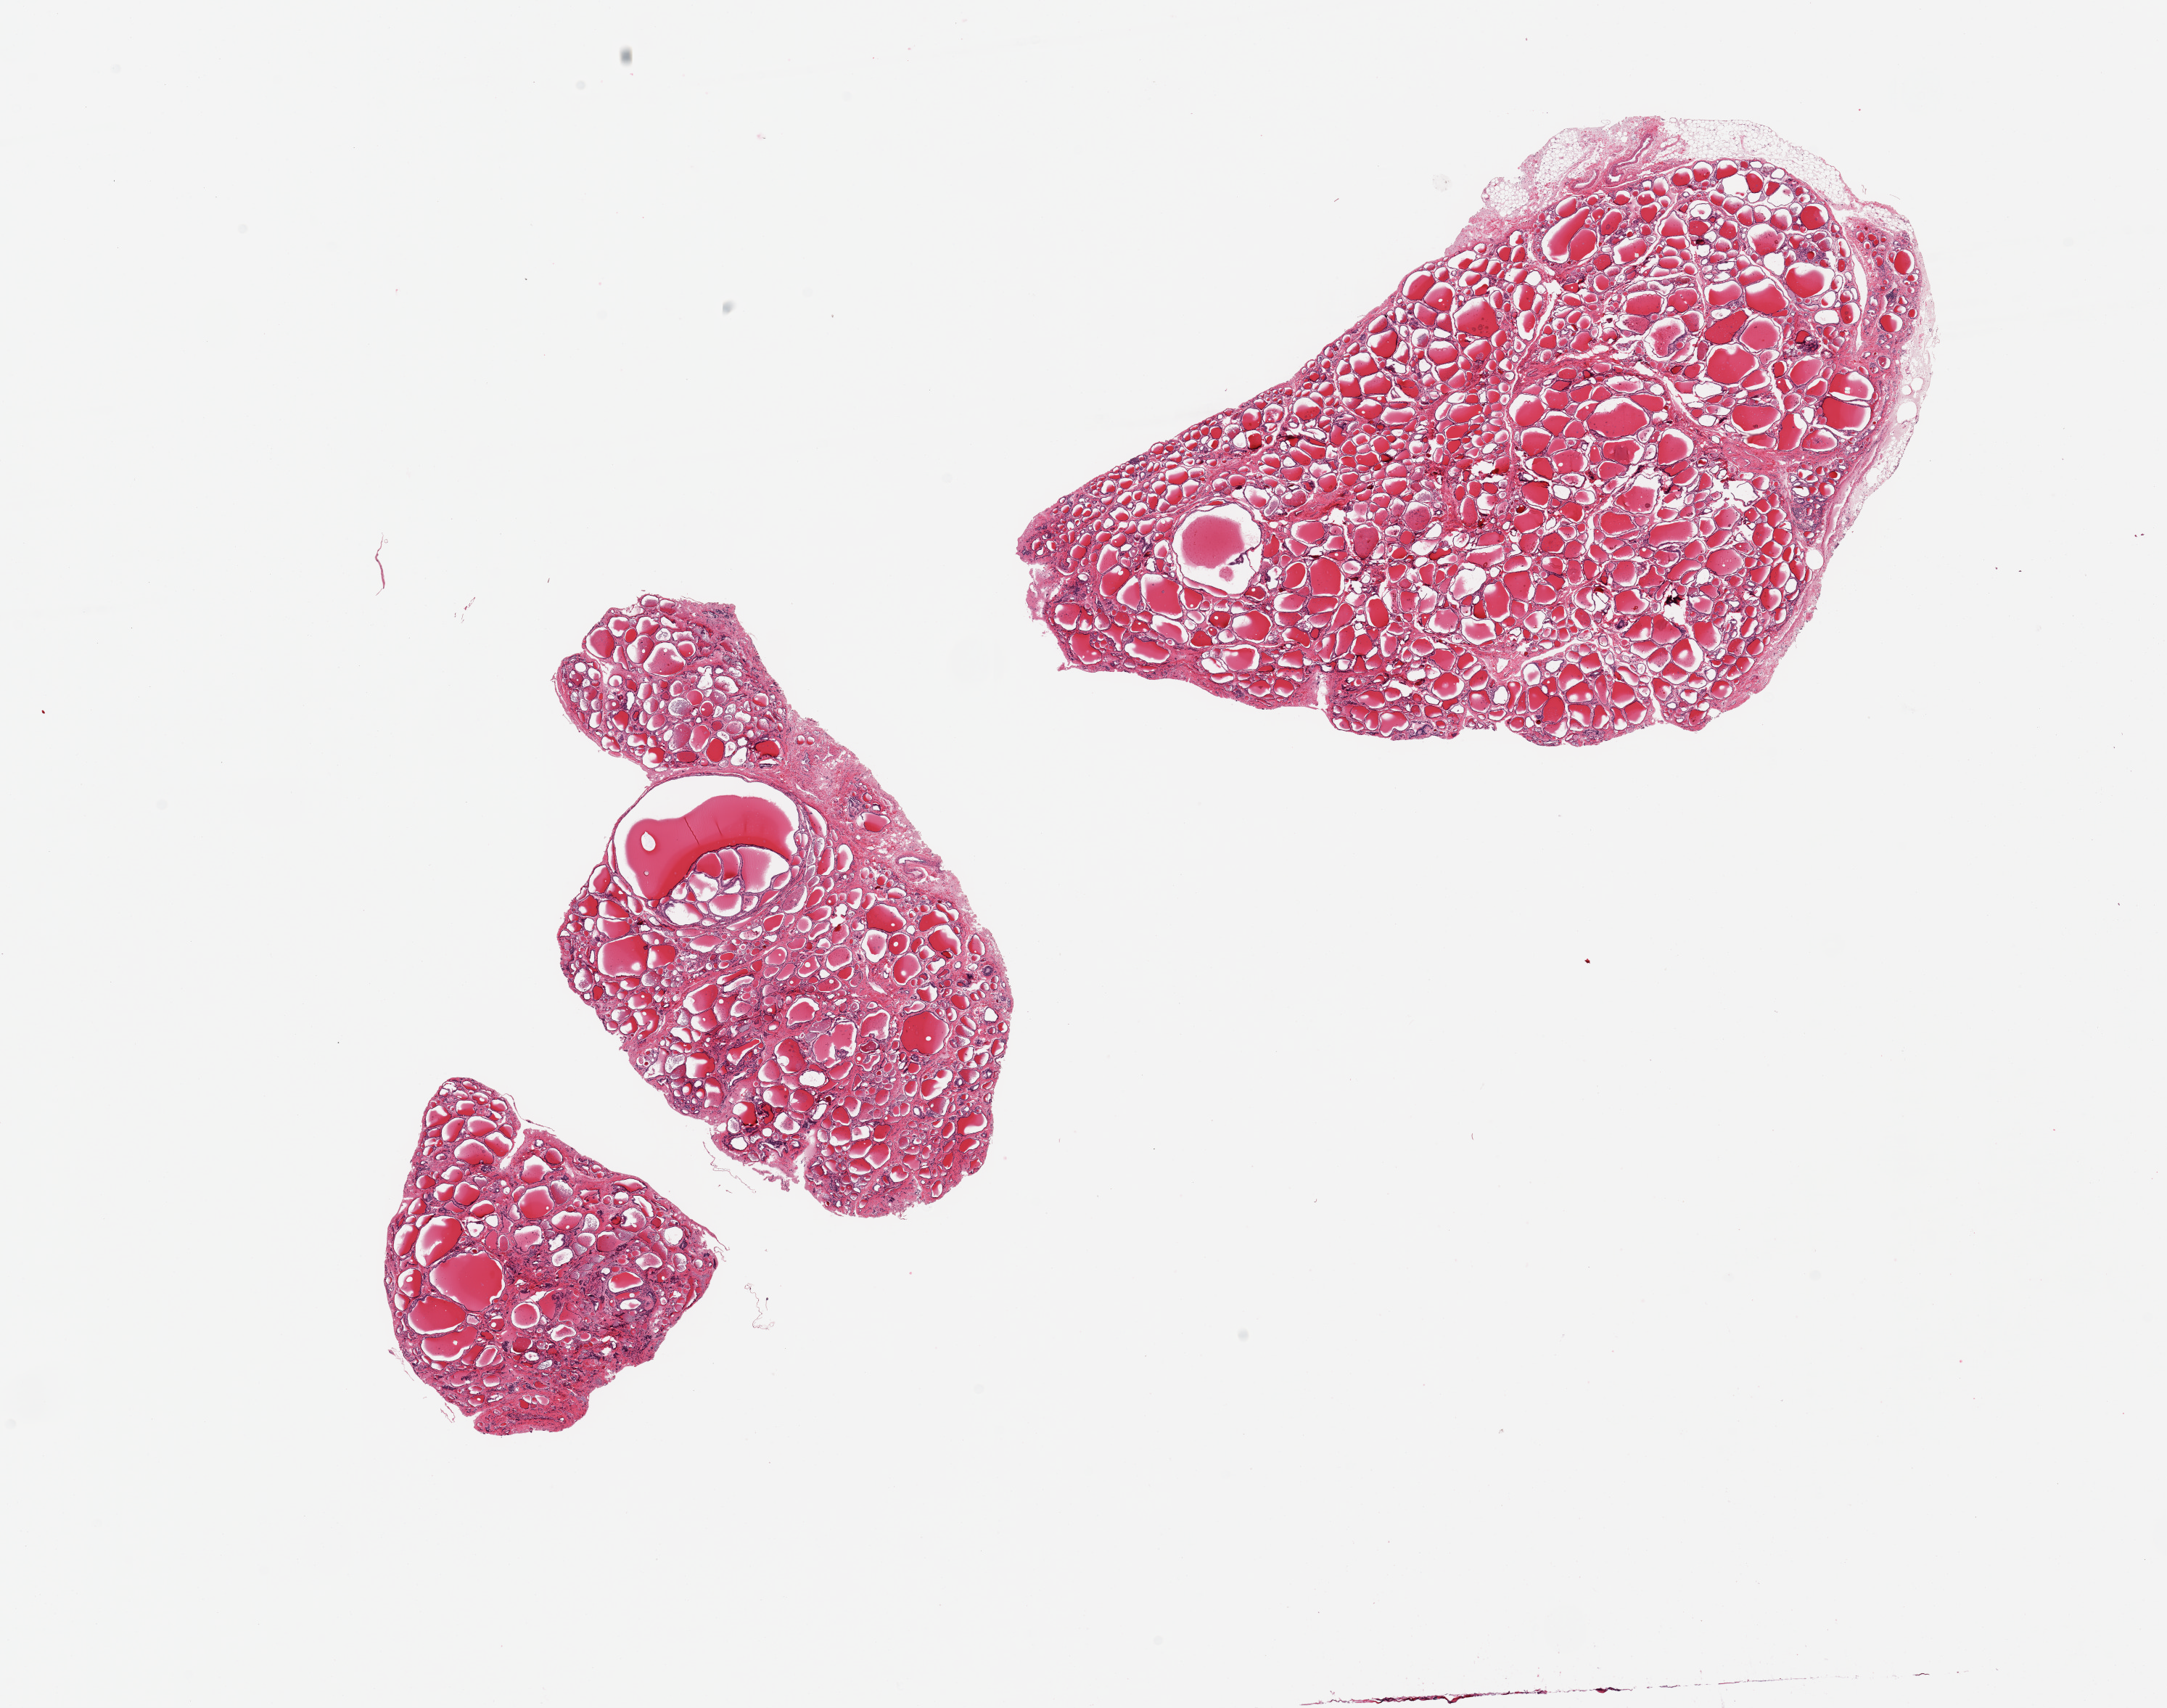
Haematoxylin and eosin whole-slide image, whole scanned area (about 23.6 x 18.6 mm) shown as a low-resolution overview; PAXgene-fixed paraffin-embedded (PFPE) section; section of thyroid (target tissue); tissue donor sample. Male donor.
Review note (as recorded): 2 pieces, mild nodular goitre, trace adhrent fat, ~0.5mm thick.